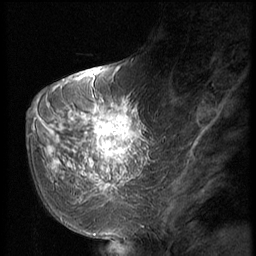
Breast MRI (dynamic contrast-enhanced), one sagittal slice. Slice 20 of 56 in the series (ordered by position). Dynamic contrast-enhanced series, image 2 of 2 at this slice position (ordered by acquisition). 1.5 T. TE 4.2 ms, TR 9 ms. 2.5 mm slice thickness. 256 × 256 image matrix, field of view 180 × 180 mm. Patient: female, 51 years. Case-level facts recorded for this patient, not image findings: setting: breast cancer imaged before/during neoadjuvant chemotherapy; receptor status: triple-negative.
Outlined on this slice (semi-automatically segmented with operator editing):
- analysis volume of interest (the breast-tissue region the enhancement analysis was run in; not a lesion): box from (x=60, y=98) to (x=147, y=197) px
- tumour enhancement mask (voxels above the 140 % enhancement threshold inside the analysis volume of interest): (x=68, y=104)–(x=141, y=193)